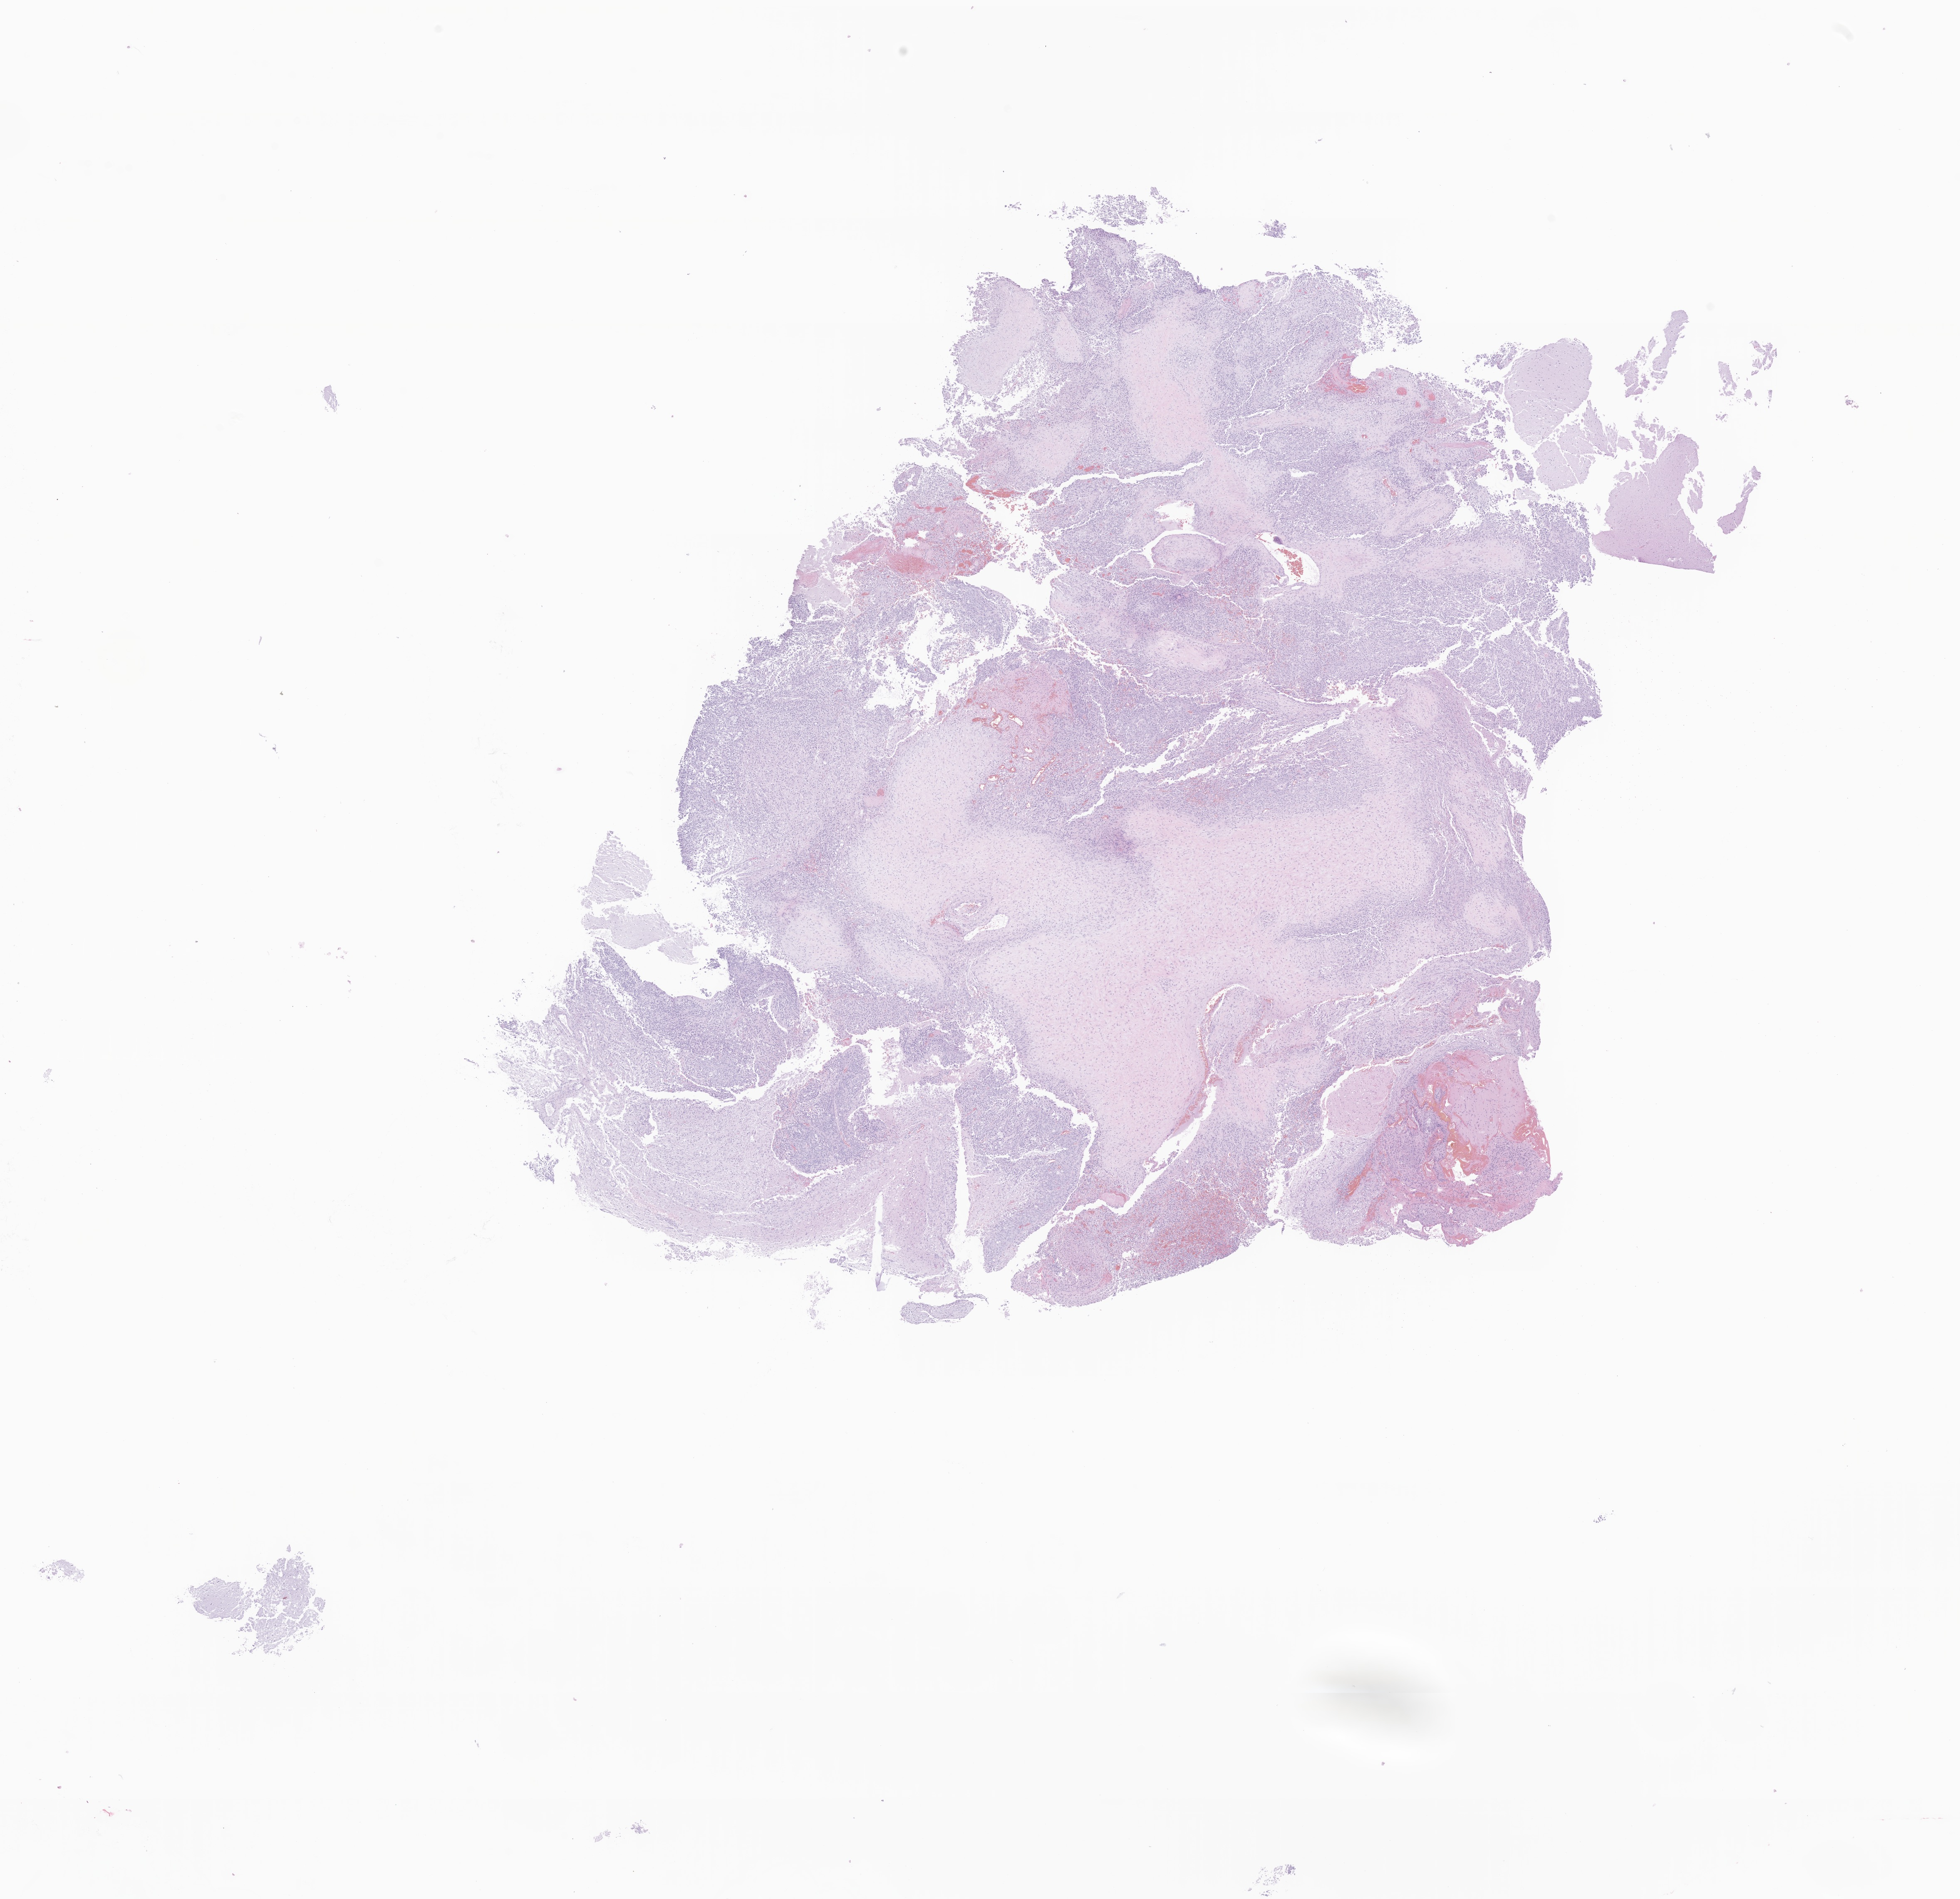
Whole-slide image, H&E stain of tumor tissue from the frontal lobe, low-resolution overview of the scanned area, about 19.9 x 19.2 mm. FFPE section. Male patient, age 151 months (12 years 7 months).
- diagnosis: Neoplasm, uncertain whether benign or malignant